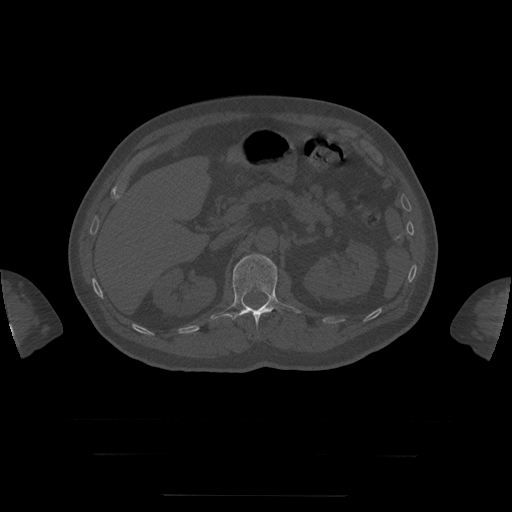
CT including the spine, one axial slice; slice 50 of 397 in the series (ordered by position); 120 kVp; bone window (W 1800 / L 400 HU); 1.25 mm slice thickness; 512 × 512 image matrix, field of view 510 × 510 mm. Patient age 73 years. Case-level facts recorded for this patient, not image findings: primary cancer: prostate.
Outlined on this slice (semi-automatic segmentation, software-assisted and operator-edited):
- L1 vertebra: bounding box [x1, y1, x2, y2] px = [211, 255, 301, 326]
- T8 vertebra: [235, 307, 249, 319]